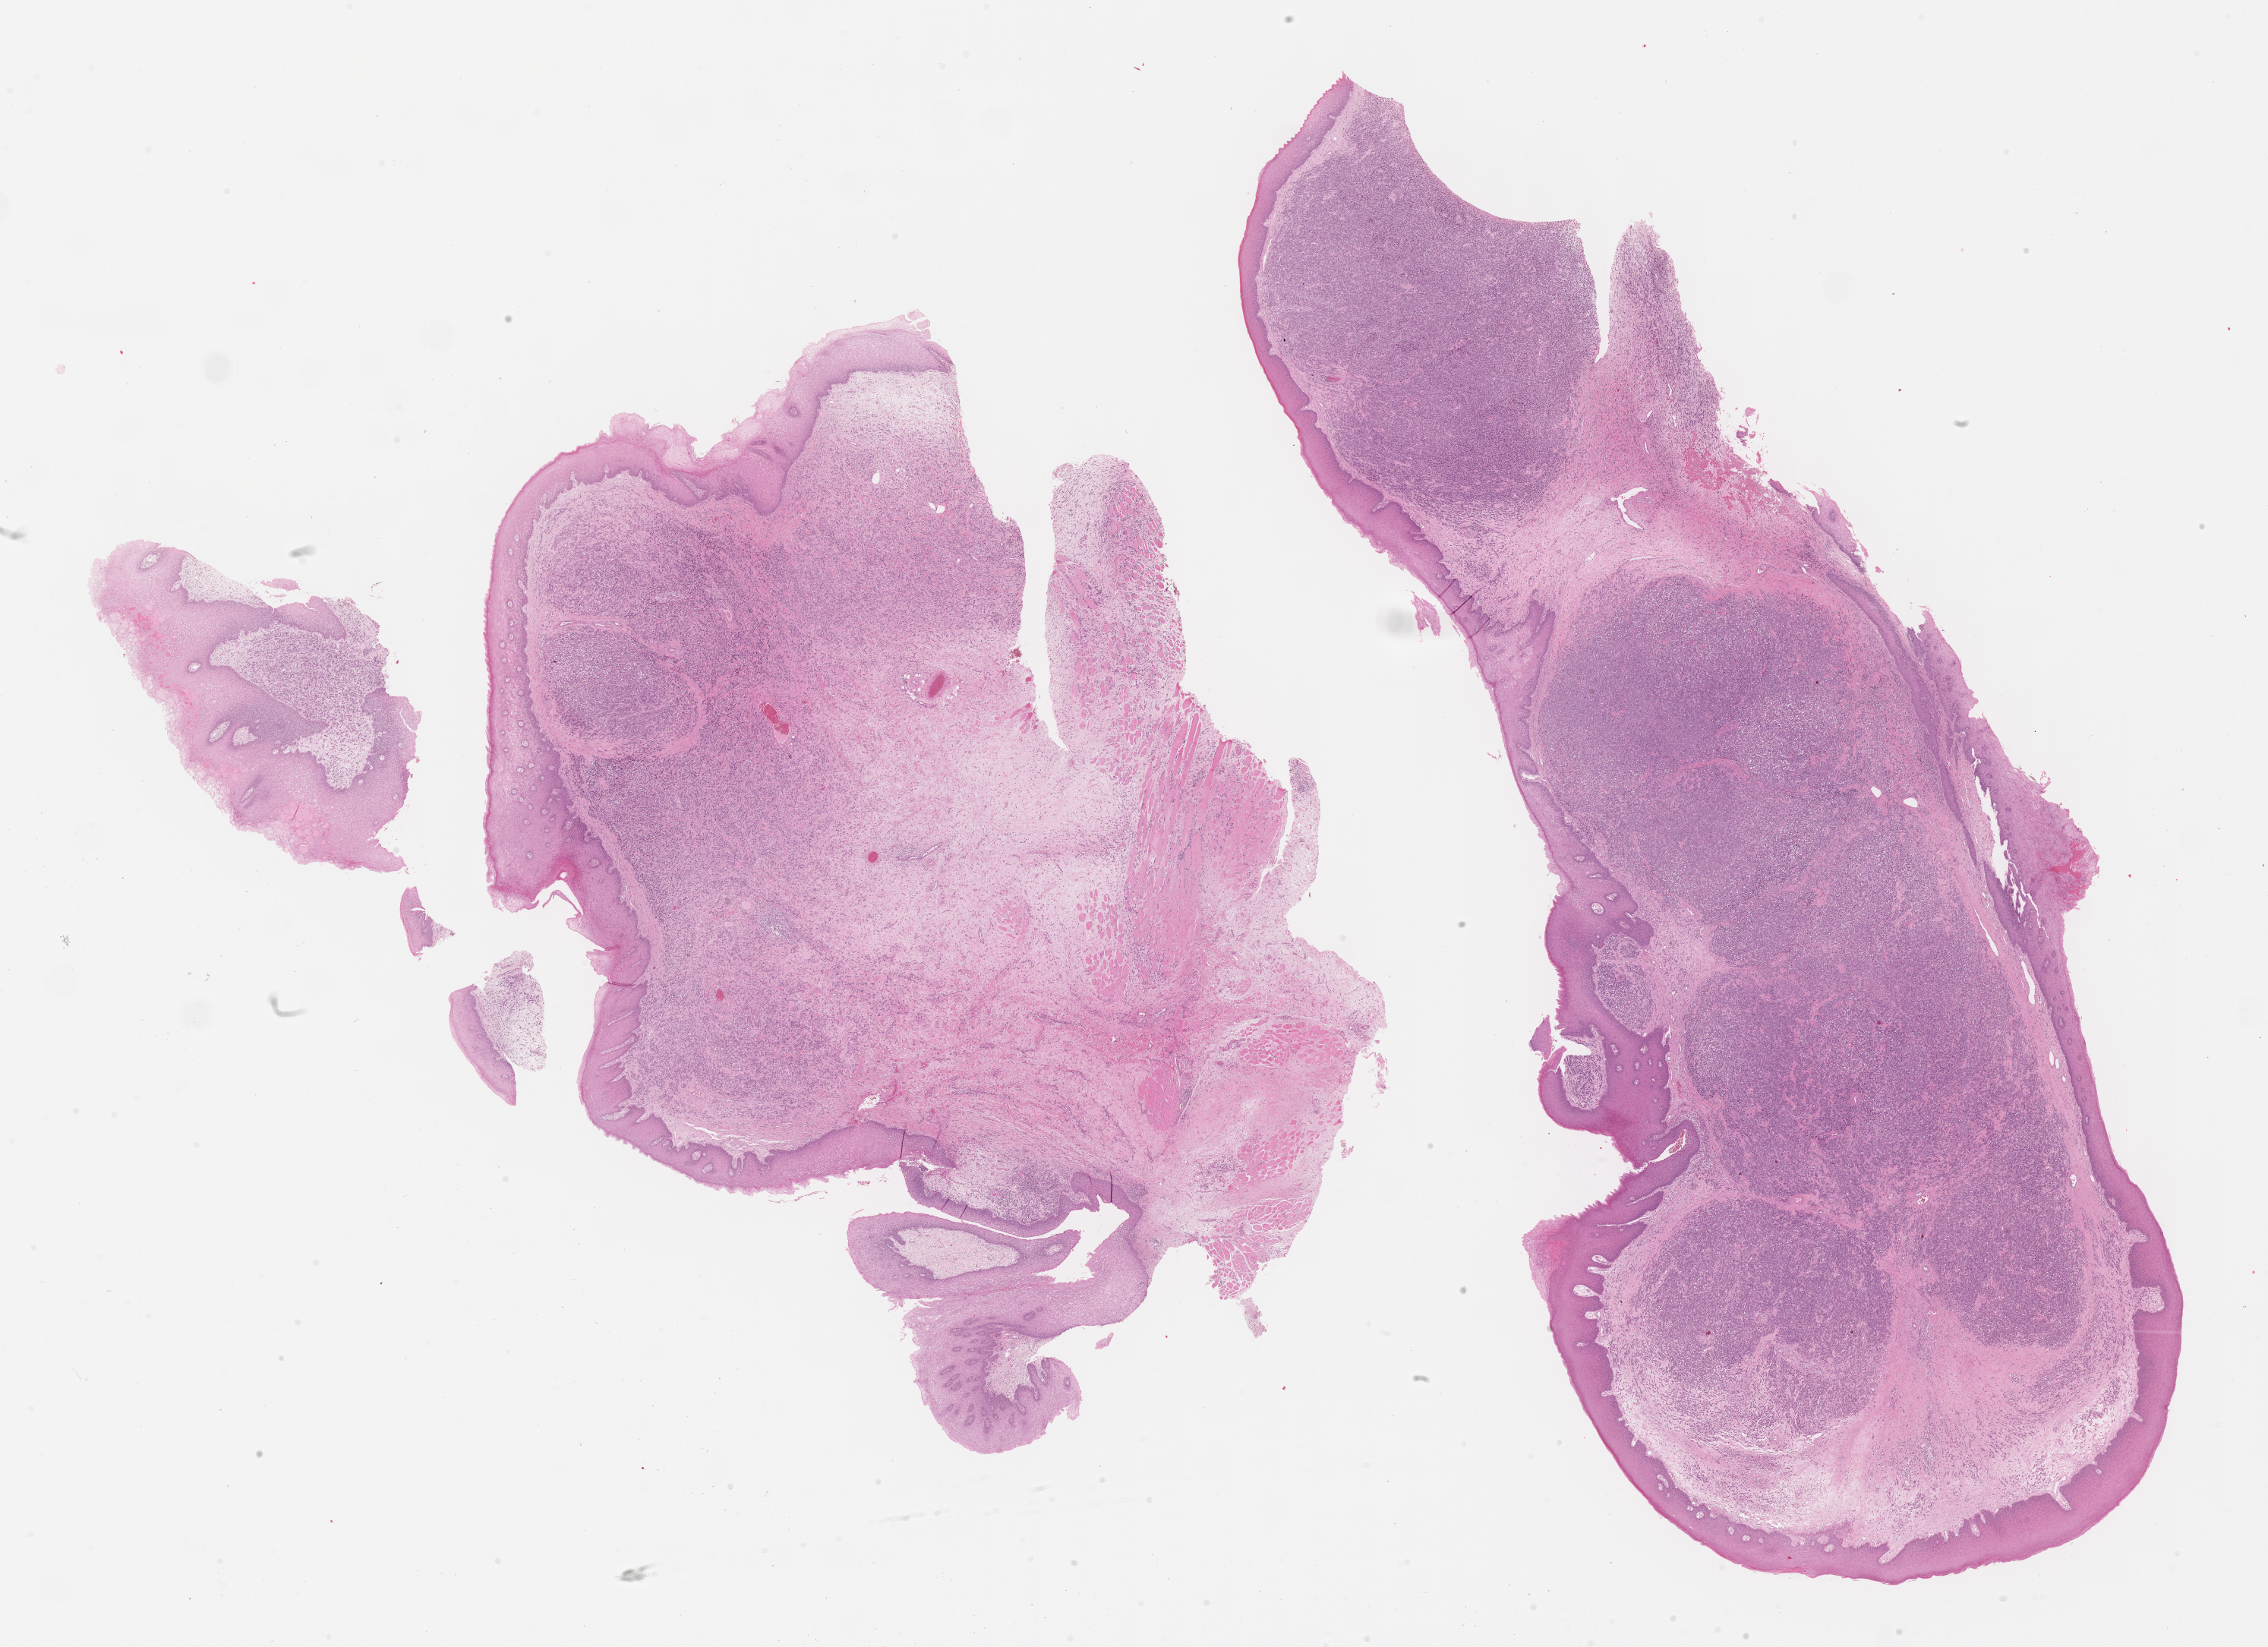
Whole-slide image, H&E stain of tumor tissue, shown as a low-resolution overview of the whole scanned area (about 24.2 x 17.5 mm), FFPE section, sample anatomic site: soft tissue - mouth, left. Male patient, age at diagnosis 16.6 years.
Diagnosis: rhabdomyosarcoma; histological classification: embryonal rhabdomyosarcoma.